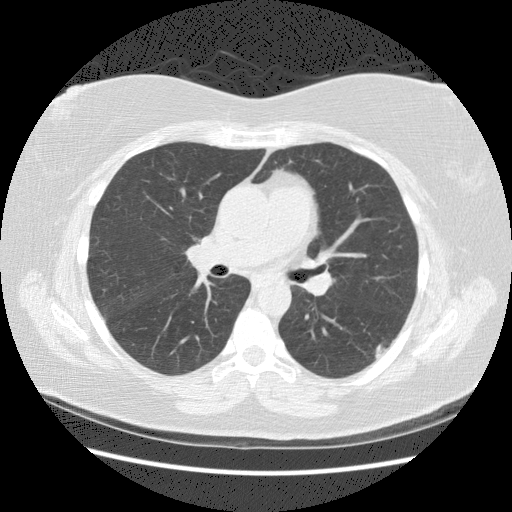
Low-dose screening chest CT, axial slice; second screening round (one year after baseline); lung window (W 1500 / L -600 HU); 2.5 mm slice thickness; slice 80 of 140 in the series; 512 × 512 image matrix. Female participant, aged 57 years at enrolment. Current smoker at enrolment.
Expert-annotated lung lesion, bounding box <360,328,402,368> (left, top, right, bottom; pixels). Reader record for this screening exam (exam-level; its link to the box is not recorded): non-calcified nodule or mass ≥4 mm, left lower lobe, 19 × 9 mm, poorly defined margins, mixed attenuation, pre-existing on the prior screen: yes; interval growth: yes. Later outcome: lung cancer diagnosed 560 days after this screen (after the third annual screen) — squamous cell carcinoma, NOS, left lower lobe, poorly differentiated (G3), stage IB (AJCC 6th edition), 40 mm at pathology.